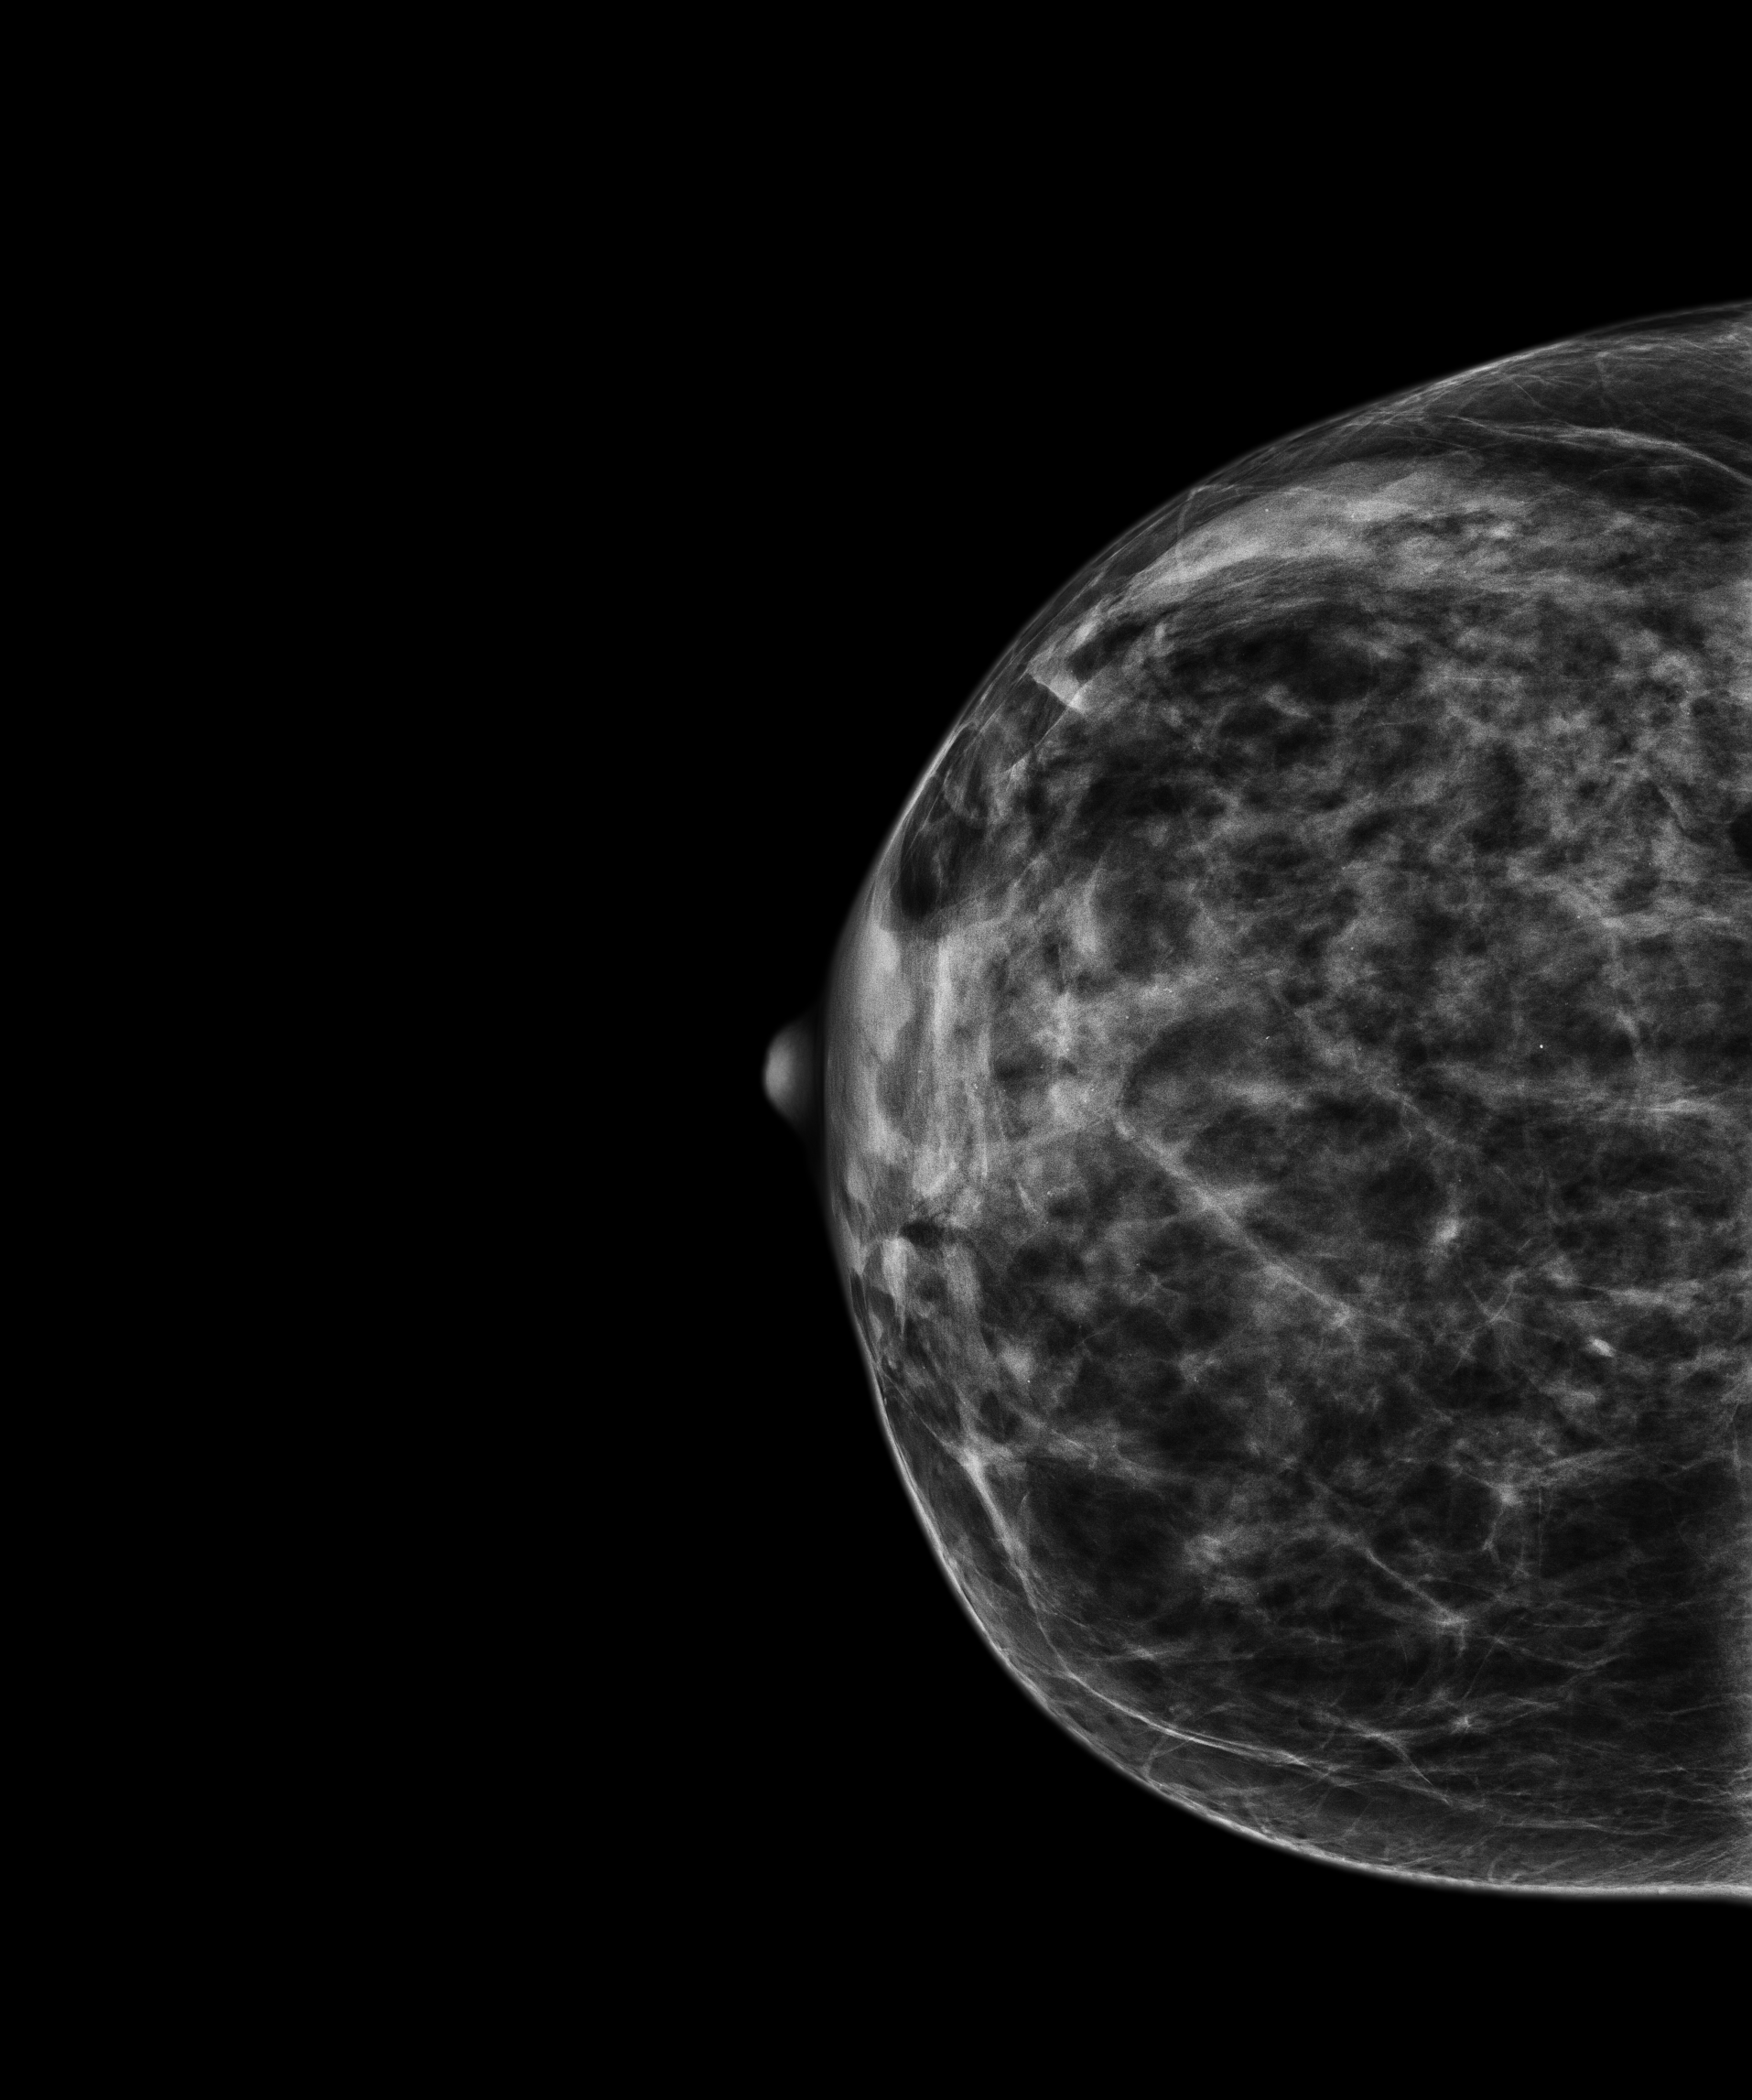
Full-field digital mammogram (FFDM), right breast, CC view, screening examination, system: Senographe Pristina. Female patient, age 47 years.
Breast density at the screening exam (both breasts): heterogeneously dense (BI-RADS density category c). Final BI-RADS category for the screening round (tomosynthesis exam, both breasts): category 3. Recall: recalled for additional imaging after this screen.